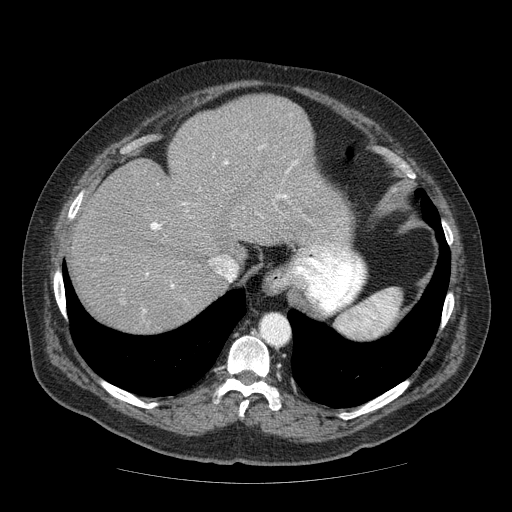
Contrast-enhanced abdominal CT (liver protocol), one axial slice; position 52 of 85 along the scan axis; 120 kVp; soft-tissue window (W 400 / L 40 HU); 2.5 mm slice thickness; 512 × 512 image matrix, field of view 420 × 420 mm. From the clinical record (not read from this slice): diagnosis: hepatocellular carcinoma (patient treated with transarterial chemoembolisation; whether this scan precedes or follows treatment is not stated here); TNM stage (as recorded): Stage-IIIA; Child-Pugh class: A; tumour size: 7 cm.
Structures marked on this image (semi-automatic segmentation, software-assisted and operator-edited):
- abdominal aorta: bounding box <260,315,289,345> (left, top, right, bottom; pixels)
- liver parenchyma outside the tumour (the mass and vessels are separate outlines, so this box may not span the whole liver): <68,94,350,332>
- liver vessels: <146,161,297,288>